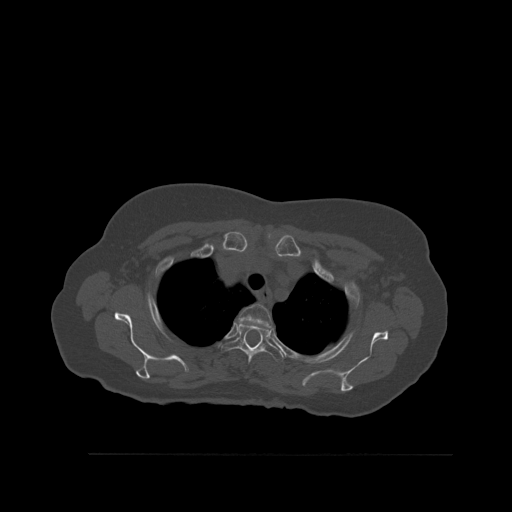
CT including the spine, one axial slice; slice 423 of 527 in the series (ordered by position); bone window (W 1800 / L 400 HU); 1.5 mm slice thickness; 512 × 512 image matrix, field of view 470 × 470 mm. Female patient, age 73 years. Case-level facts recorded for this patient, not image findings: primary cancer: breast.
Structures marked on this image (semi-automatic segmentation, software-assisted and operator-edited):
- T2 vertebra: box from (x=238, y=304) to (x=273, y=330) px
- T3 vertebra: (x=222, y=322)–(x=284, y=365)